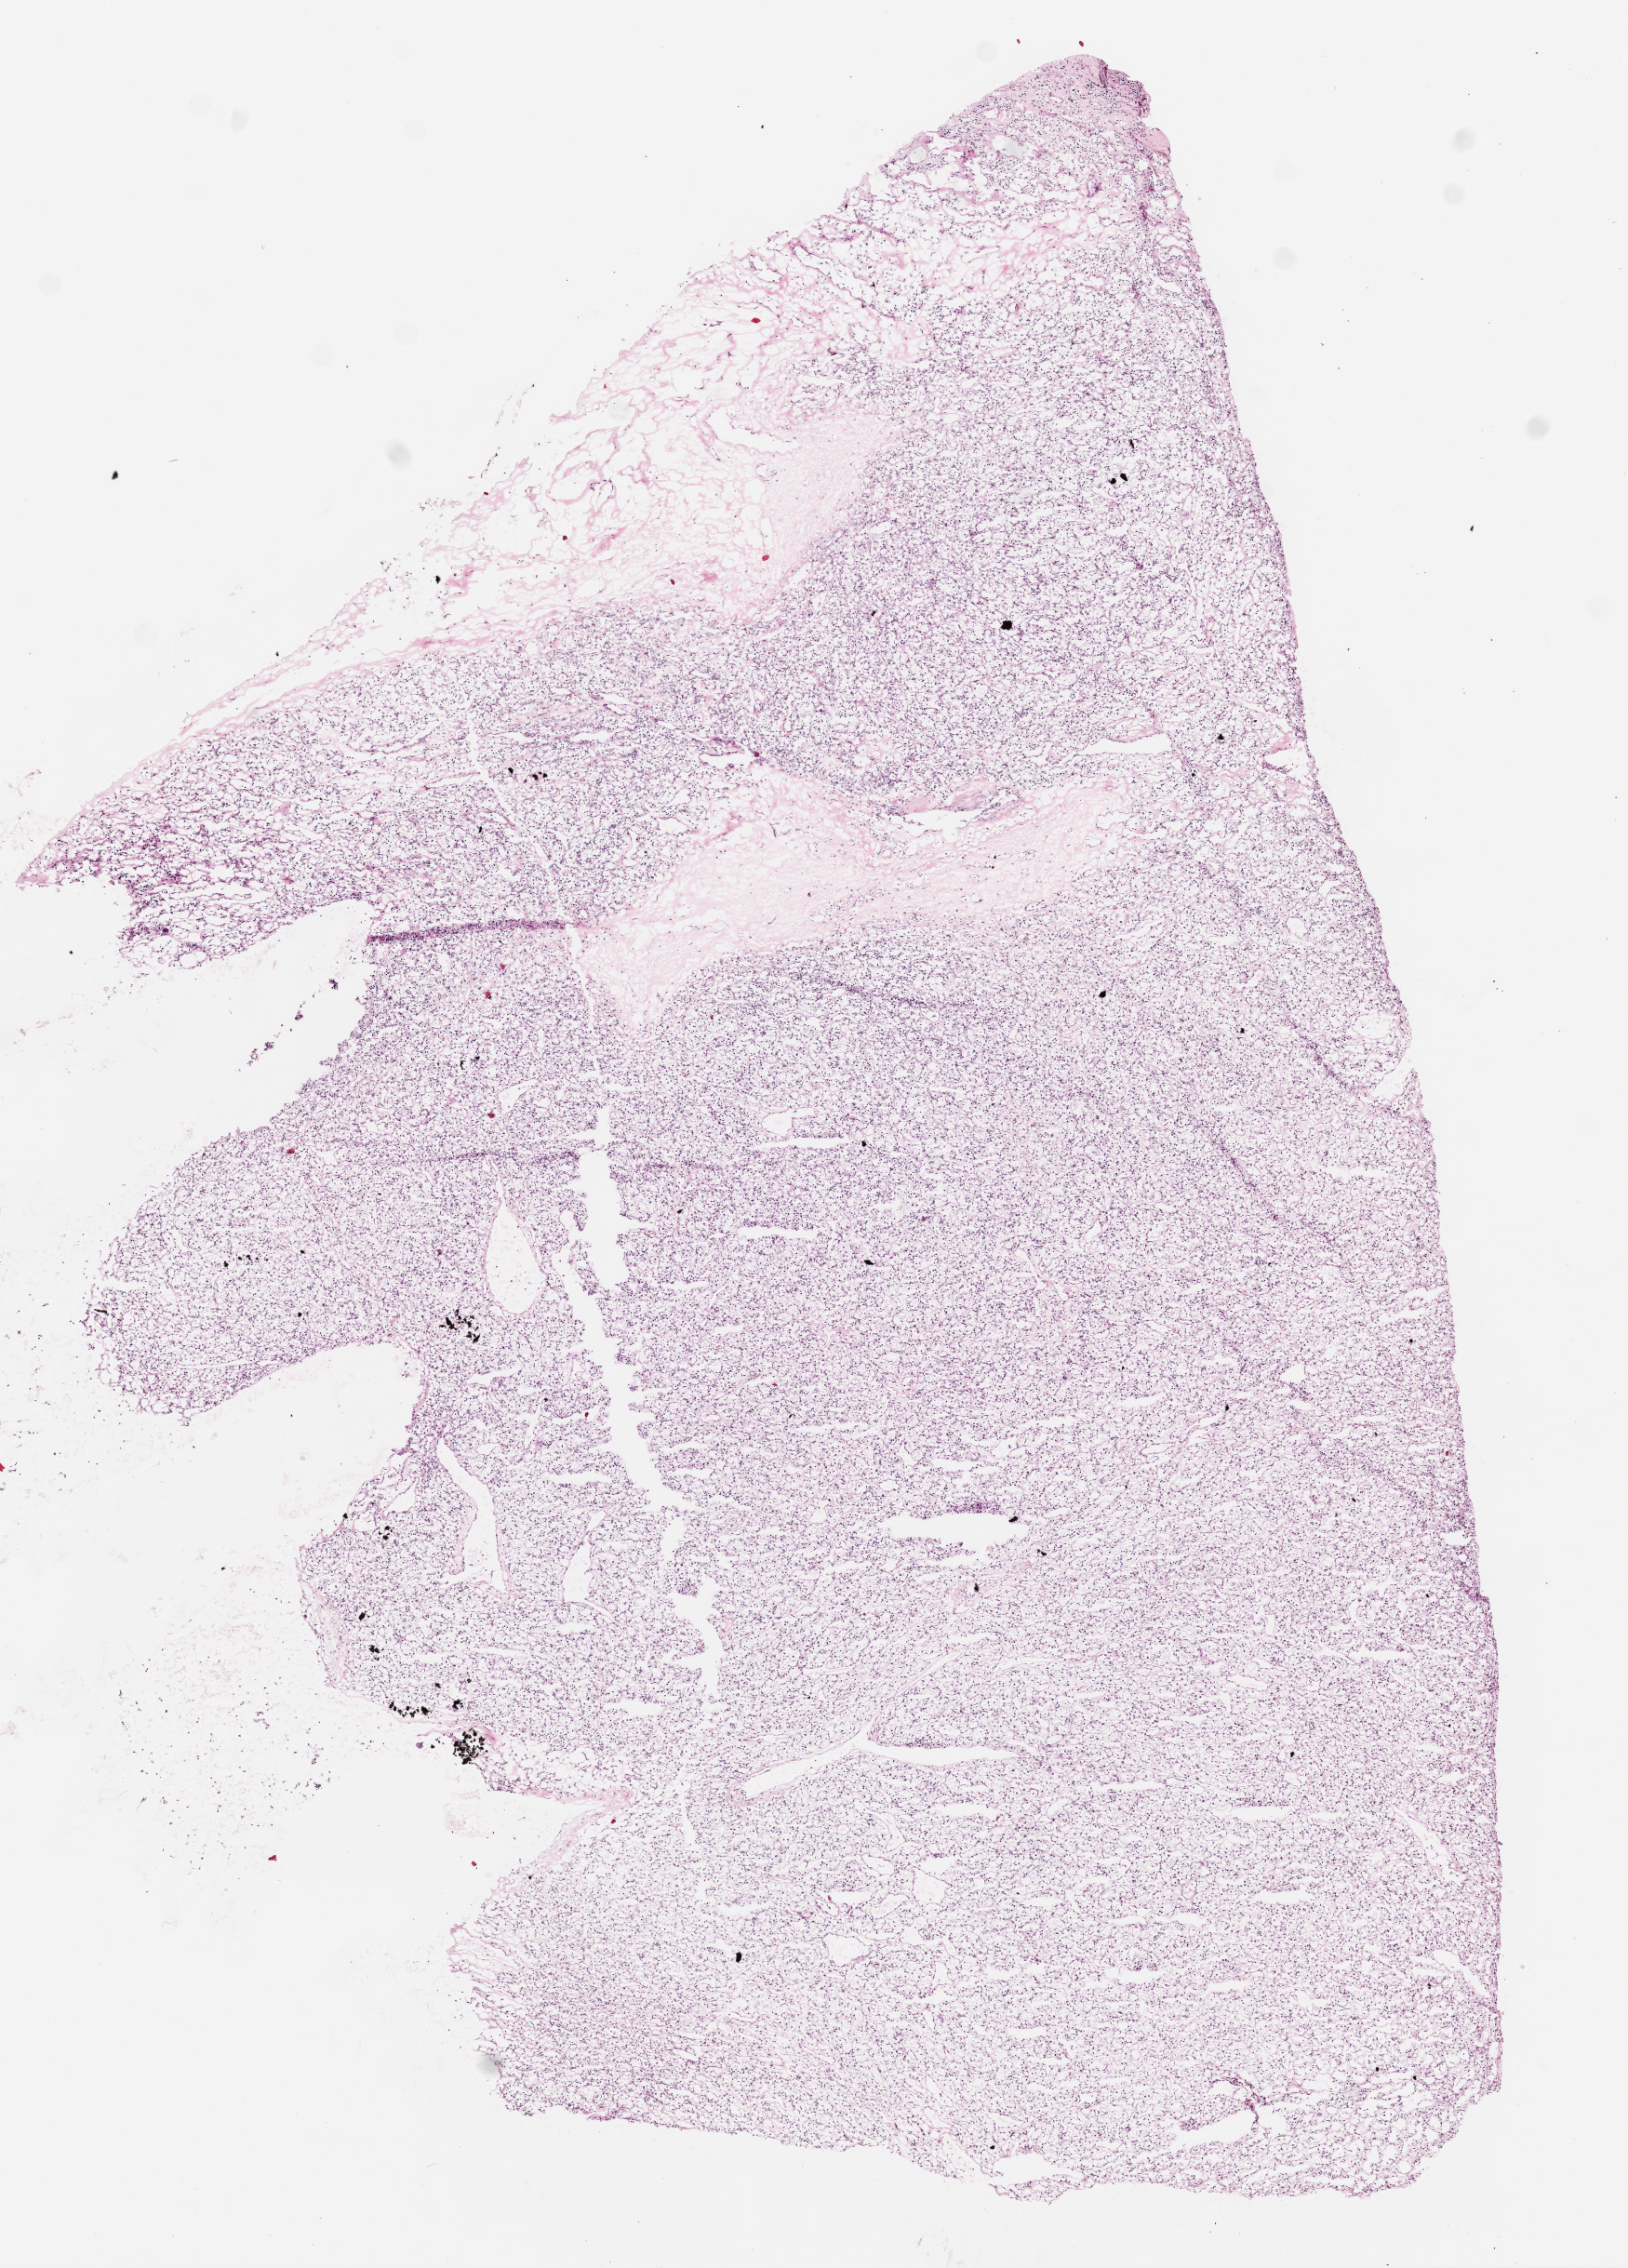
Digitized H&E-stained tissue section (whole slide), a low-resolution overview of the entire scanned area, about 7.0 x 9.8 mm (from a 20x scan). Frozen section from the top of the tissue portion. Kidney, primary tumour sample. Patient: female, age at initial diagnosis 61 years. Histologic grade: G1 (well differentiated). Composition of this section per pathologist review: tumour cells 95%, tumour nuclei 90%, normal cells 0%, stromal cells 5%, necrosis 0%. Inflammatory infiltration, as recorded: lymphocyte infiltration 0%, monocyte infiltration 0%, neutrophil infiltration 0%.
AJCC pathologic stage: II (7th edition). Histologic diagnosis: Clear cell adenocarcinoma, NOS. Laterality: right.